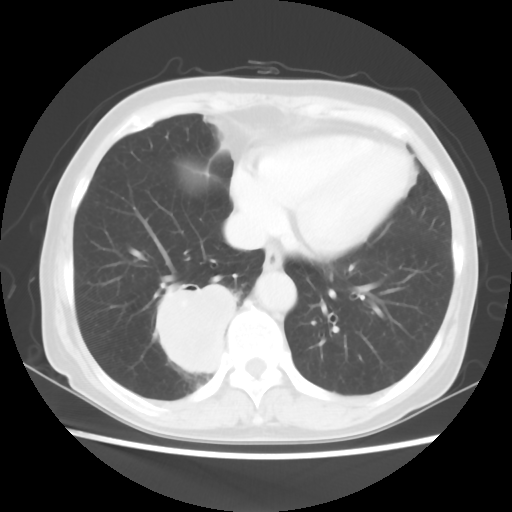
Chest CT, one axial slice. Position 17 of 56 along the scan axis. 120 kVp. Lung window (W 1500 / L -600 HU). 512 × 512 image matrix. Patient: female, 66 years. From the clinical record (not read from this slice): clinical TNM (as recorded): T2 N3 M0.
Structures marked on this image (bounding box drawn by a radiologist):
- lung tumour (recorded histology: small cell carcinoma): bounding box (x1, y1, x2, y2) in pixels: (133, 258, 231, 383)